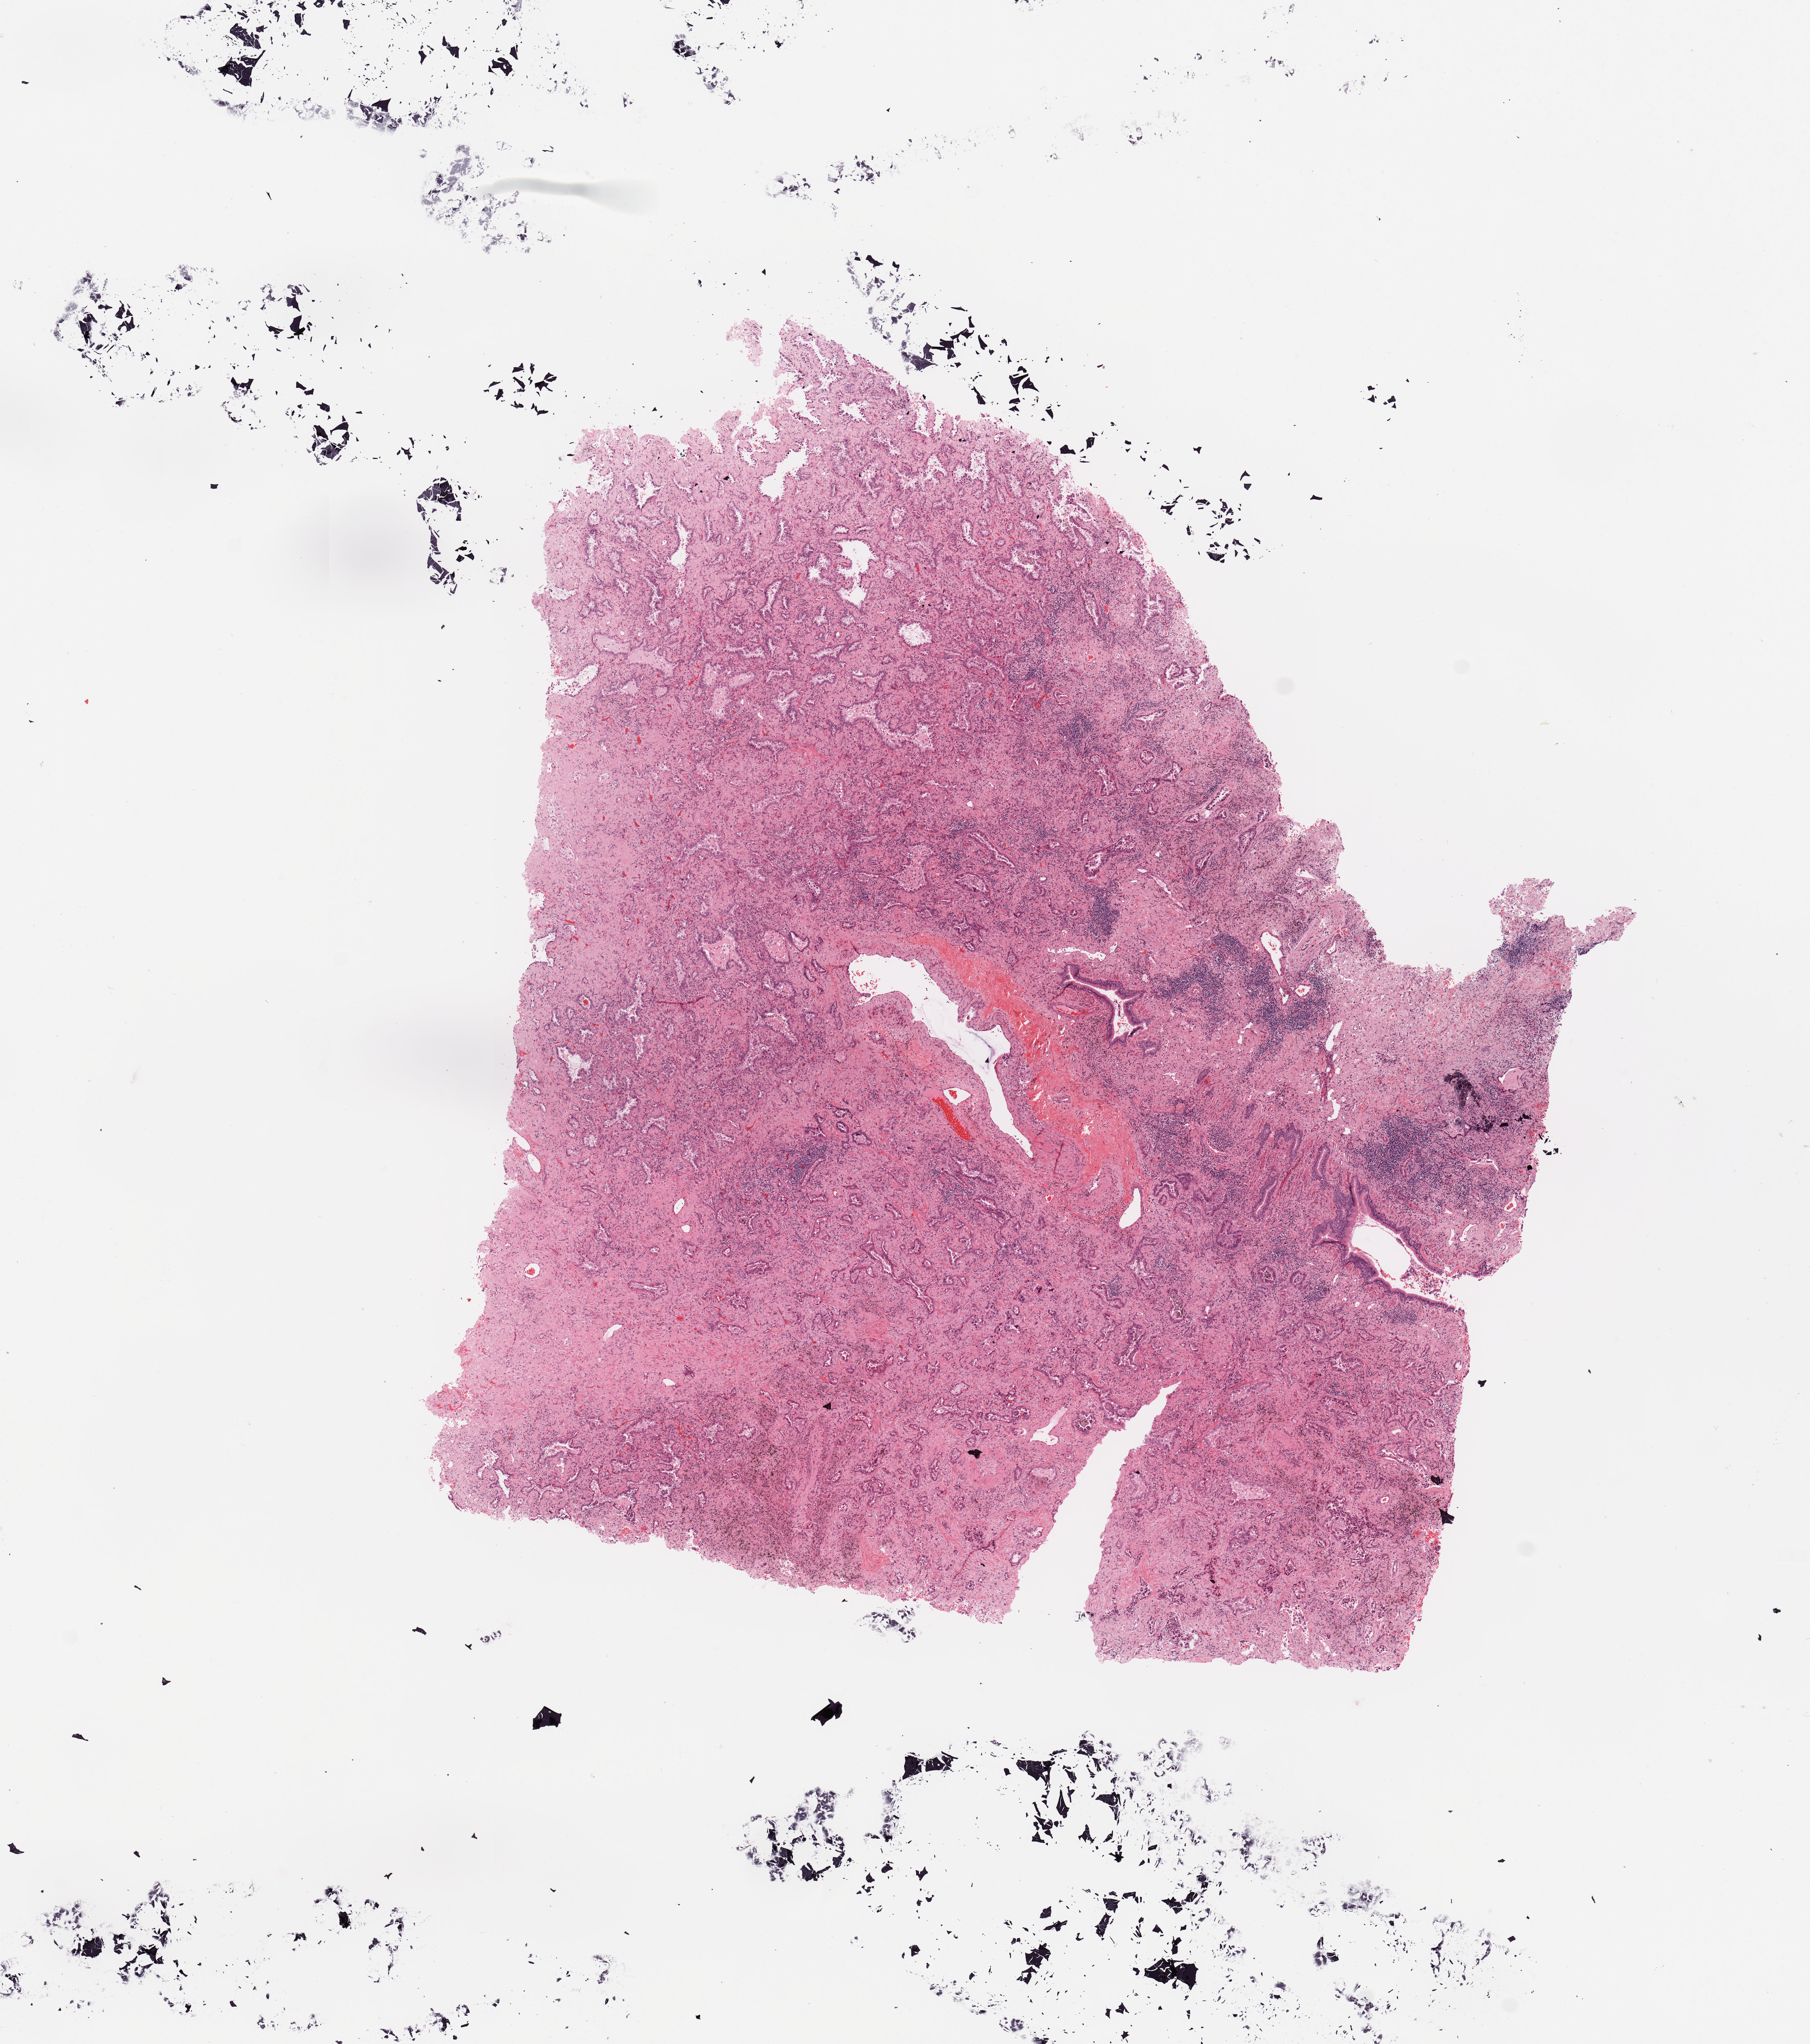
Hematoxylin and eosin (H&E) stained whole-slide image, whole scanned area (about 10.8 x 12.2 mm, acquisition: 20x scan) shown as a low-resolution overview; tumour tissue sample, sampled site: lung. 68-year-old female patient. Histologic grade: G2 (moderately differentiated). Pathologist review of this section (percent, as recorded): tumour nuclei 65%, necrosis 5%.
Histologic diagnosis: Adenocarcinoma, NOS. AJCC pathologic stage: IA. Primary tumour site (as recorded): right upper lobe.